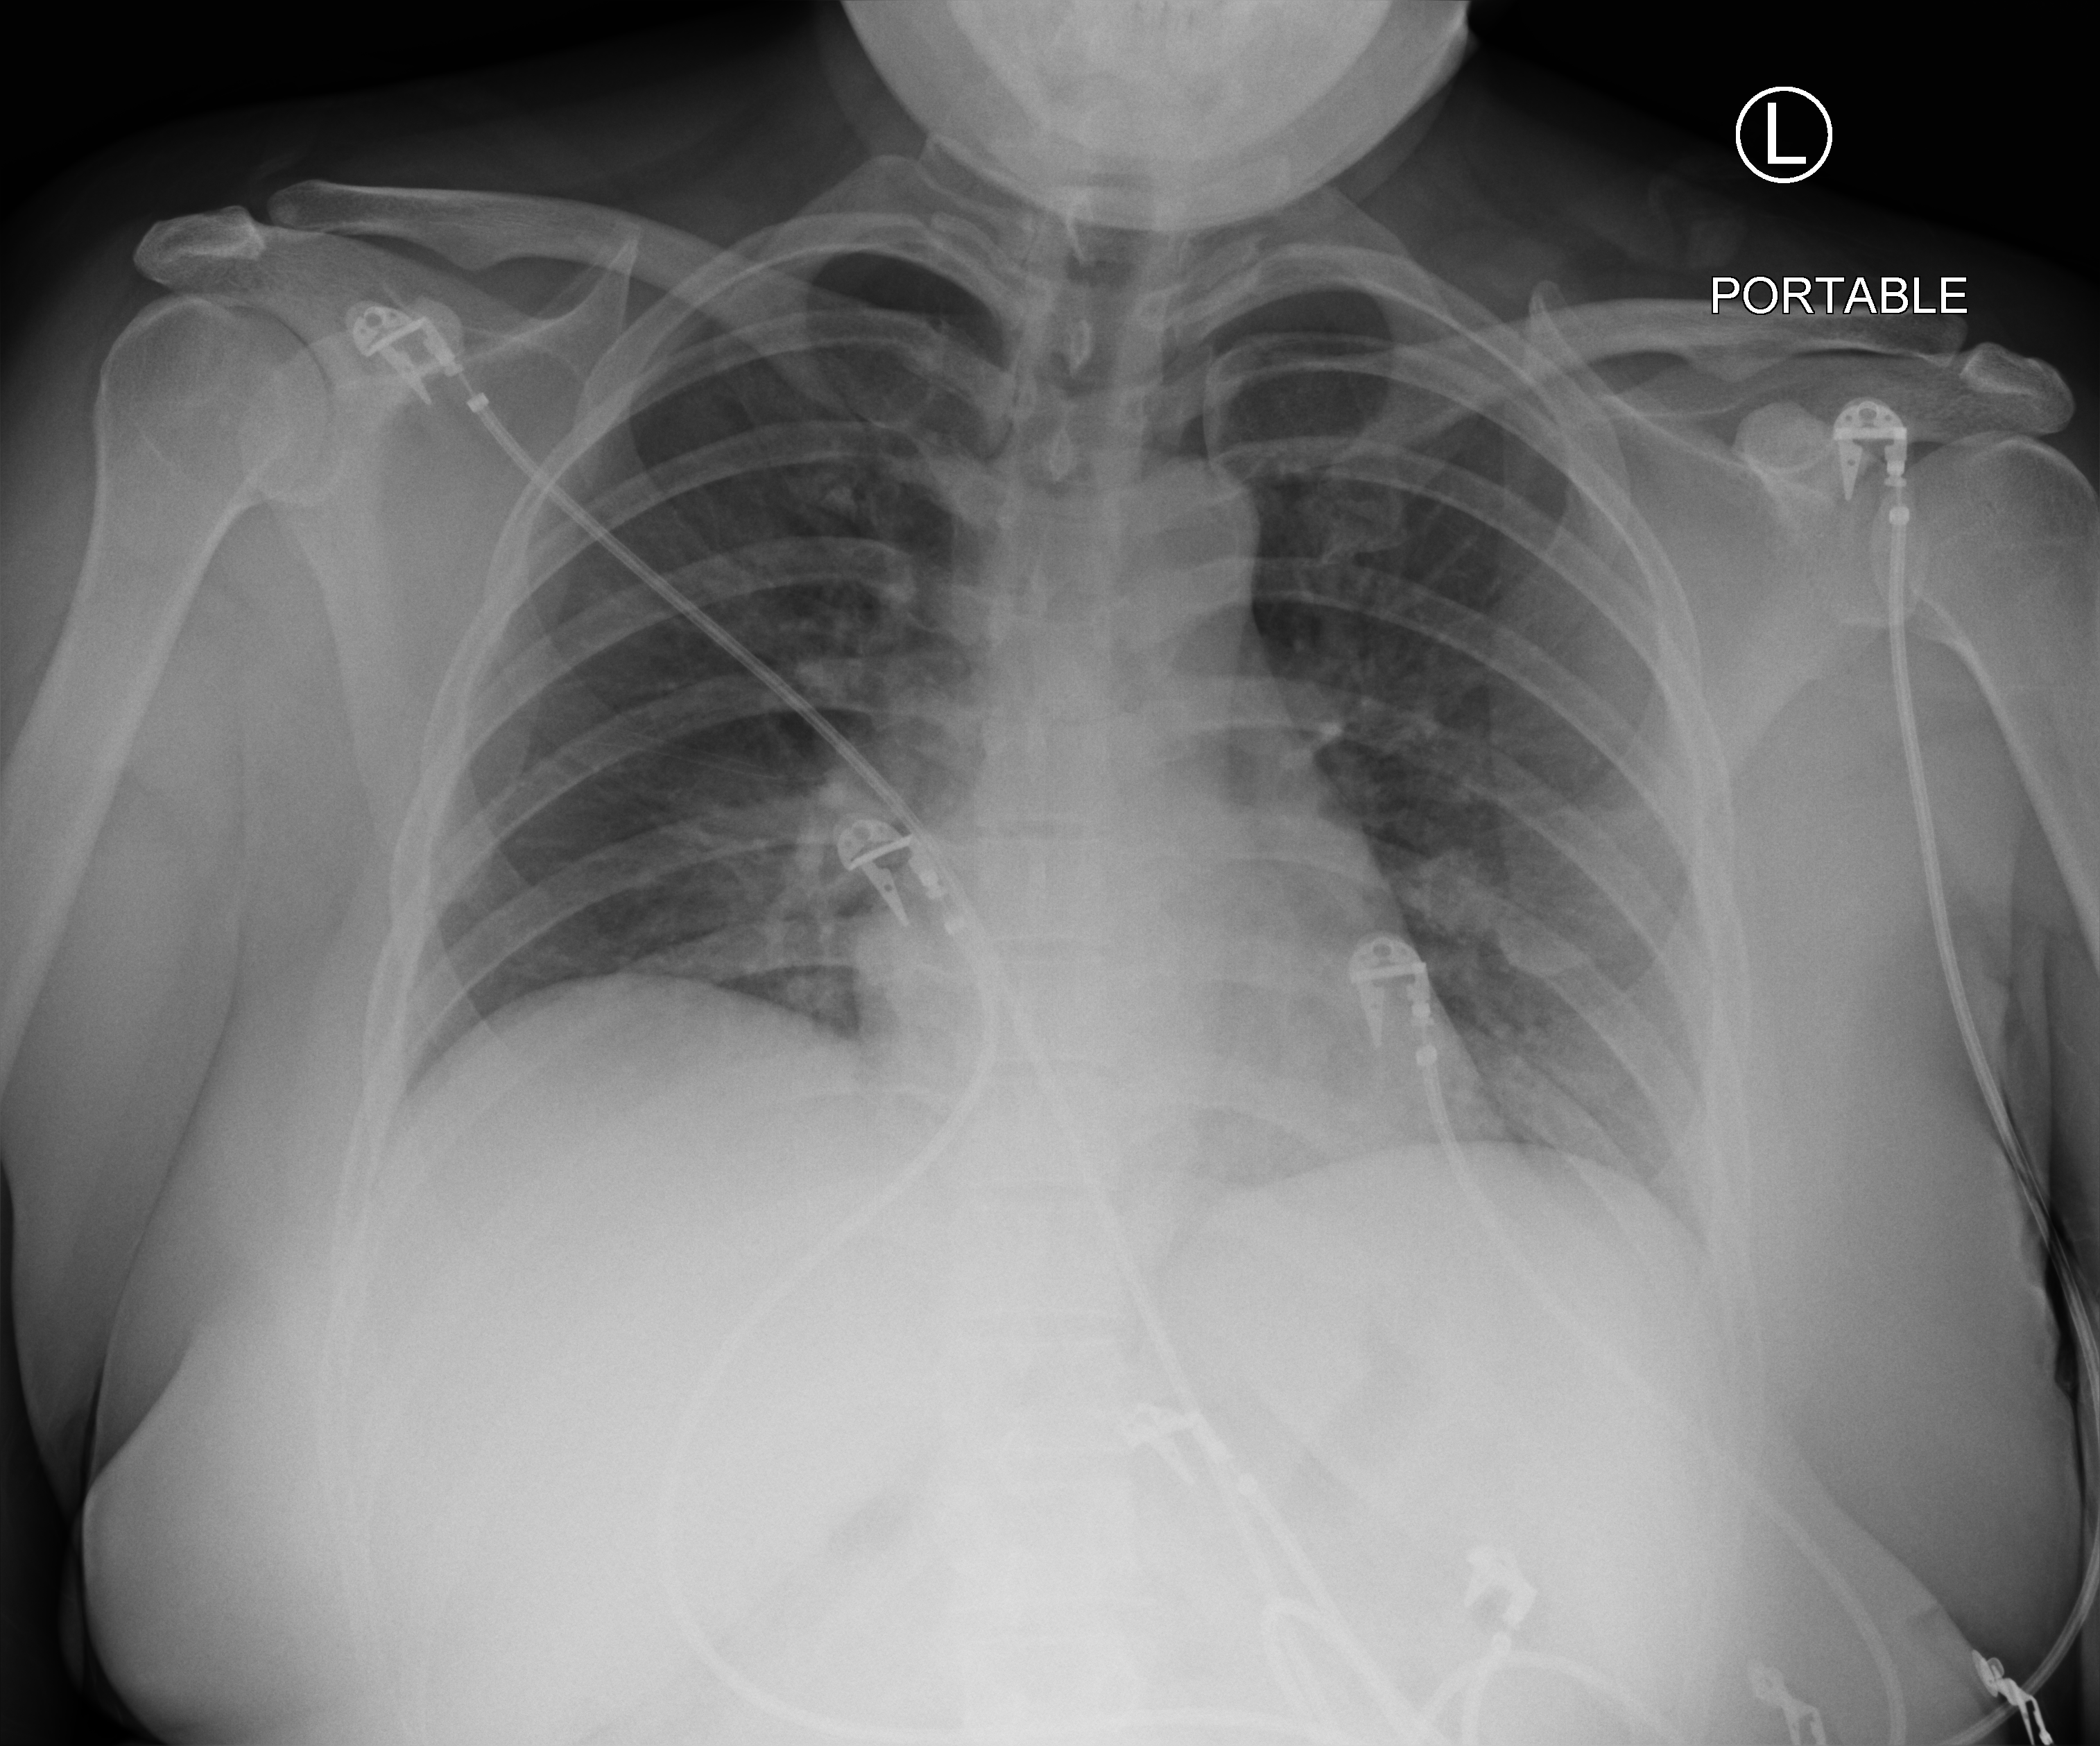
Portable chest radiograph; anteroposterior (AP) projection. Female patient hospitalised with COVID-19, age 18–59 years.
Admission-level facts for this patient (not findings on this image; timing relative to this image not recorded): length of hospital stay: 4 days; diabetes (admission record): no.